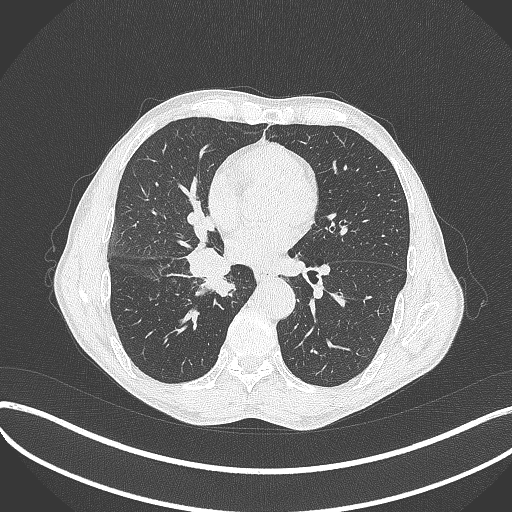
Chest CT, one axial slice; slice 202 of 481 in the series (ordered by position); reconstruction kernel B70f; 120 kVp; lung window (W 1500 / L -600 HU); 512 × 512 image matrix, field of view 400 × 400 mm. Male patient, age 65 years. Case-level facts recorded for this patient, not image findings: clinical TNM (as recorded): T2a N0 M0; histopathological grade: G2.
Annotated regions visible in this slice (rectangle marked by the reading radiologist):
- lung tumour (recorded histology: squamous cell carcinoma): bounding box [x1, y1, x2, y2] px = [180, 242, 242, 304]